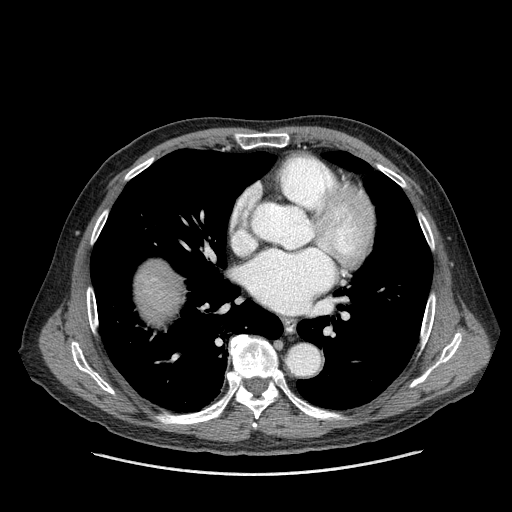
Contrast-enhanced abdominal CT (liver protocol), one axial slice; position 166 of 180 along the scan axis; reconstruction kernel STANDARD; 120 kVp; one of 2 acquisitions stored at this slice position; soft-tissue window (W 400 / L 40 HU); 2.5 mm slice thickness; 512 × 512 image matrix, field of view 420 × 420 mm. From the clinical record (not read from this slice): diagnosis: hepatocellular carcinoma (patient treated with transarterial chemoembolisation; whether this scan precedes or follows treatment is not stated here); TNM stage (as recorded): Stage-II; Child-Pugh class: A; tumour differentiation: well differentiated; tumour size: 2.8 cm.
Outlined on this slice (semi-automatically segmented with operator editing):
- liver parenchyma outside the tumour (the mass and vessels are separate outlines, so this box may not span the whole liver): box from (x=134, y=260) to (x=184, y=324) px
- mass: (x=140, y=274)–(x=162, y=296)